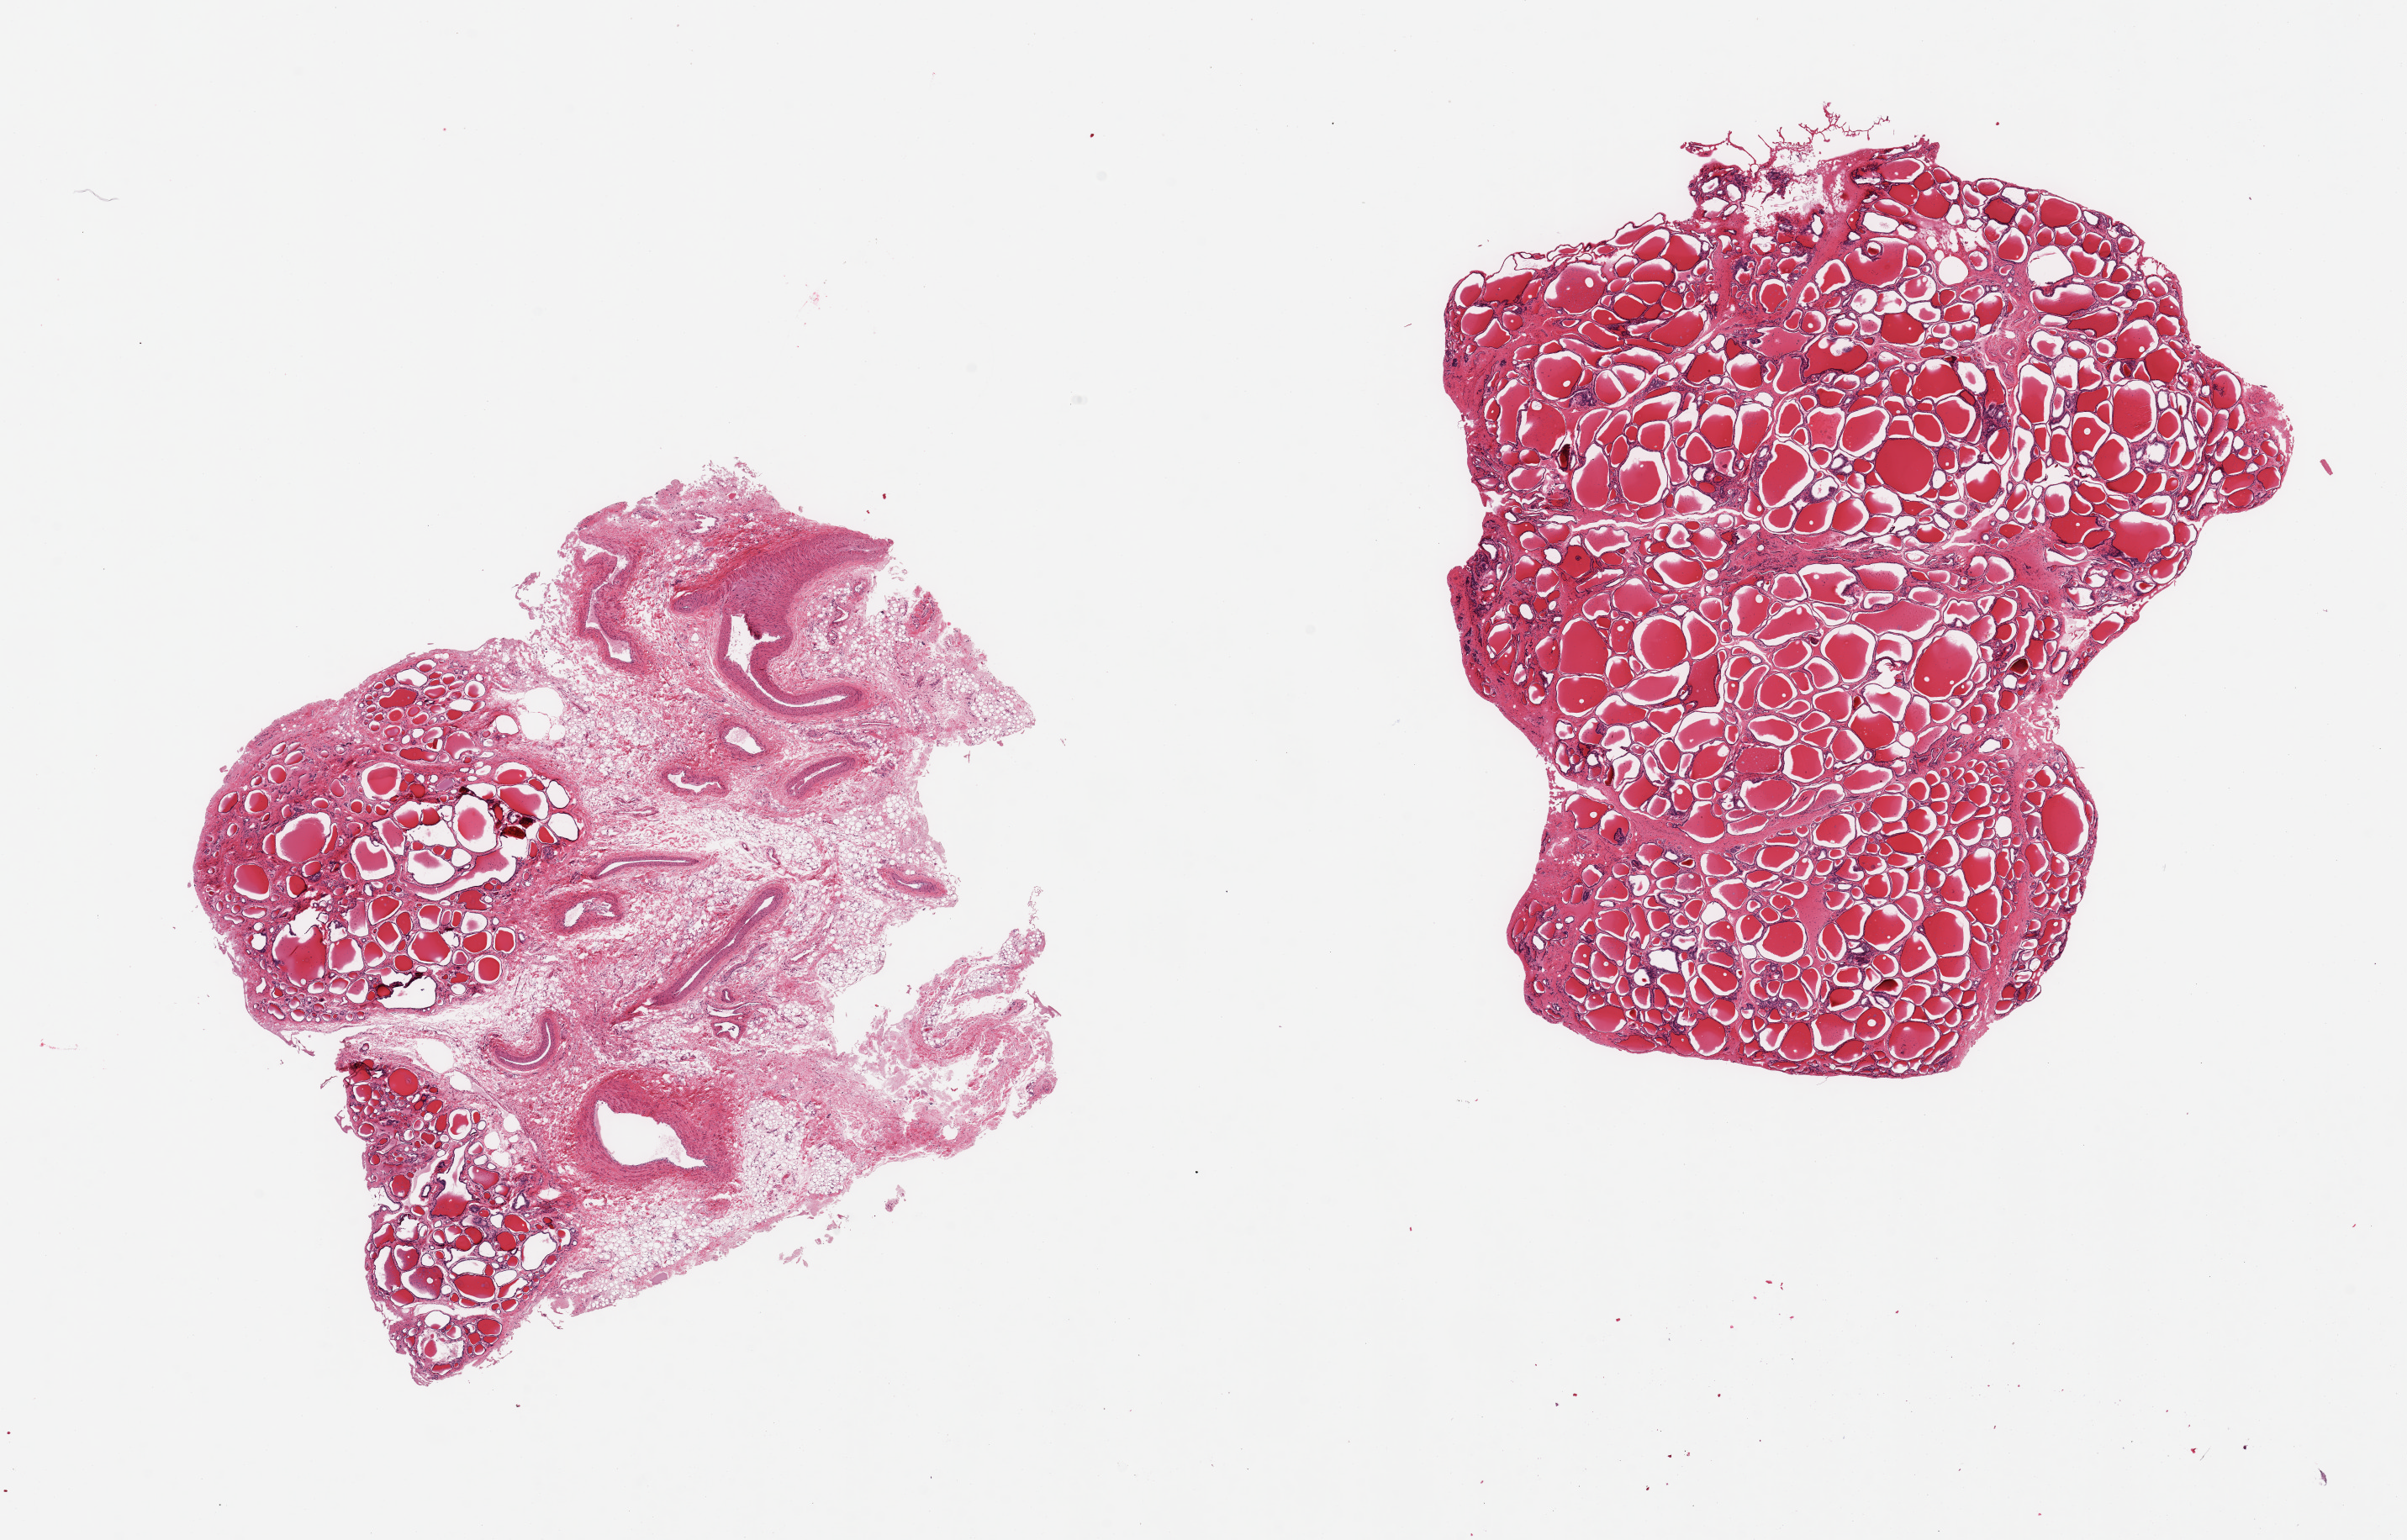
Digitized H&E-stained section, brightfield, shown as a low-resolution overview of the whole scanned area (about 22.6 x 14.5 mm, from a 20x scan), PAXgene-fixed paraffin-embedded (PFPE) section, section of thyroid (target tissue), tissue donor sample. Donor sex: male.
- pathologist's review note for this sample: 2 pieces; 1 piece contains 60% fibrovascular stroma